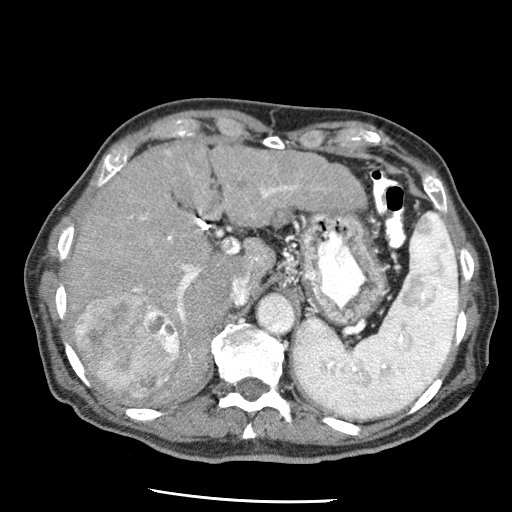
Contrast-enhanced abdominal CT (liver protocol), one axial slice. Slice 40 of 79 in the series (ordered by position). Reconstruction kernel STANDARD. Soft-tissue window (W 400 / L 40 HU). 2.5 mm slice thickness. 512 × 512 image matrix, field of view 320 × 320 mm. From the clinical record (not read from this slice): diagnosis: hepatocellular carcinoma (patient treated with transarterial chemoembolisation; whether this scan precedes or follows treatment is not stated here); TNM stage (as recorded): Stage-IIIA; Child-Pugh class: A; tumour differentiation: moderately differentiated; tumour nodularity: multinodular.
Structures marked on this image (semi-automatic segmentation, software-assisted and operator-edited):
- liver parenchyma outside the tumour (the mass and vessels are separate outlines, so this box may not span the whole liver): bounding box [x1, y1, x2, y2] px = [64, 144, 296, 404]
- mass: [75, 290, 179, 398]
- liver vessels: [128, 151, 288, 362]